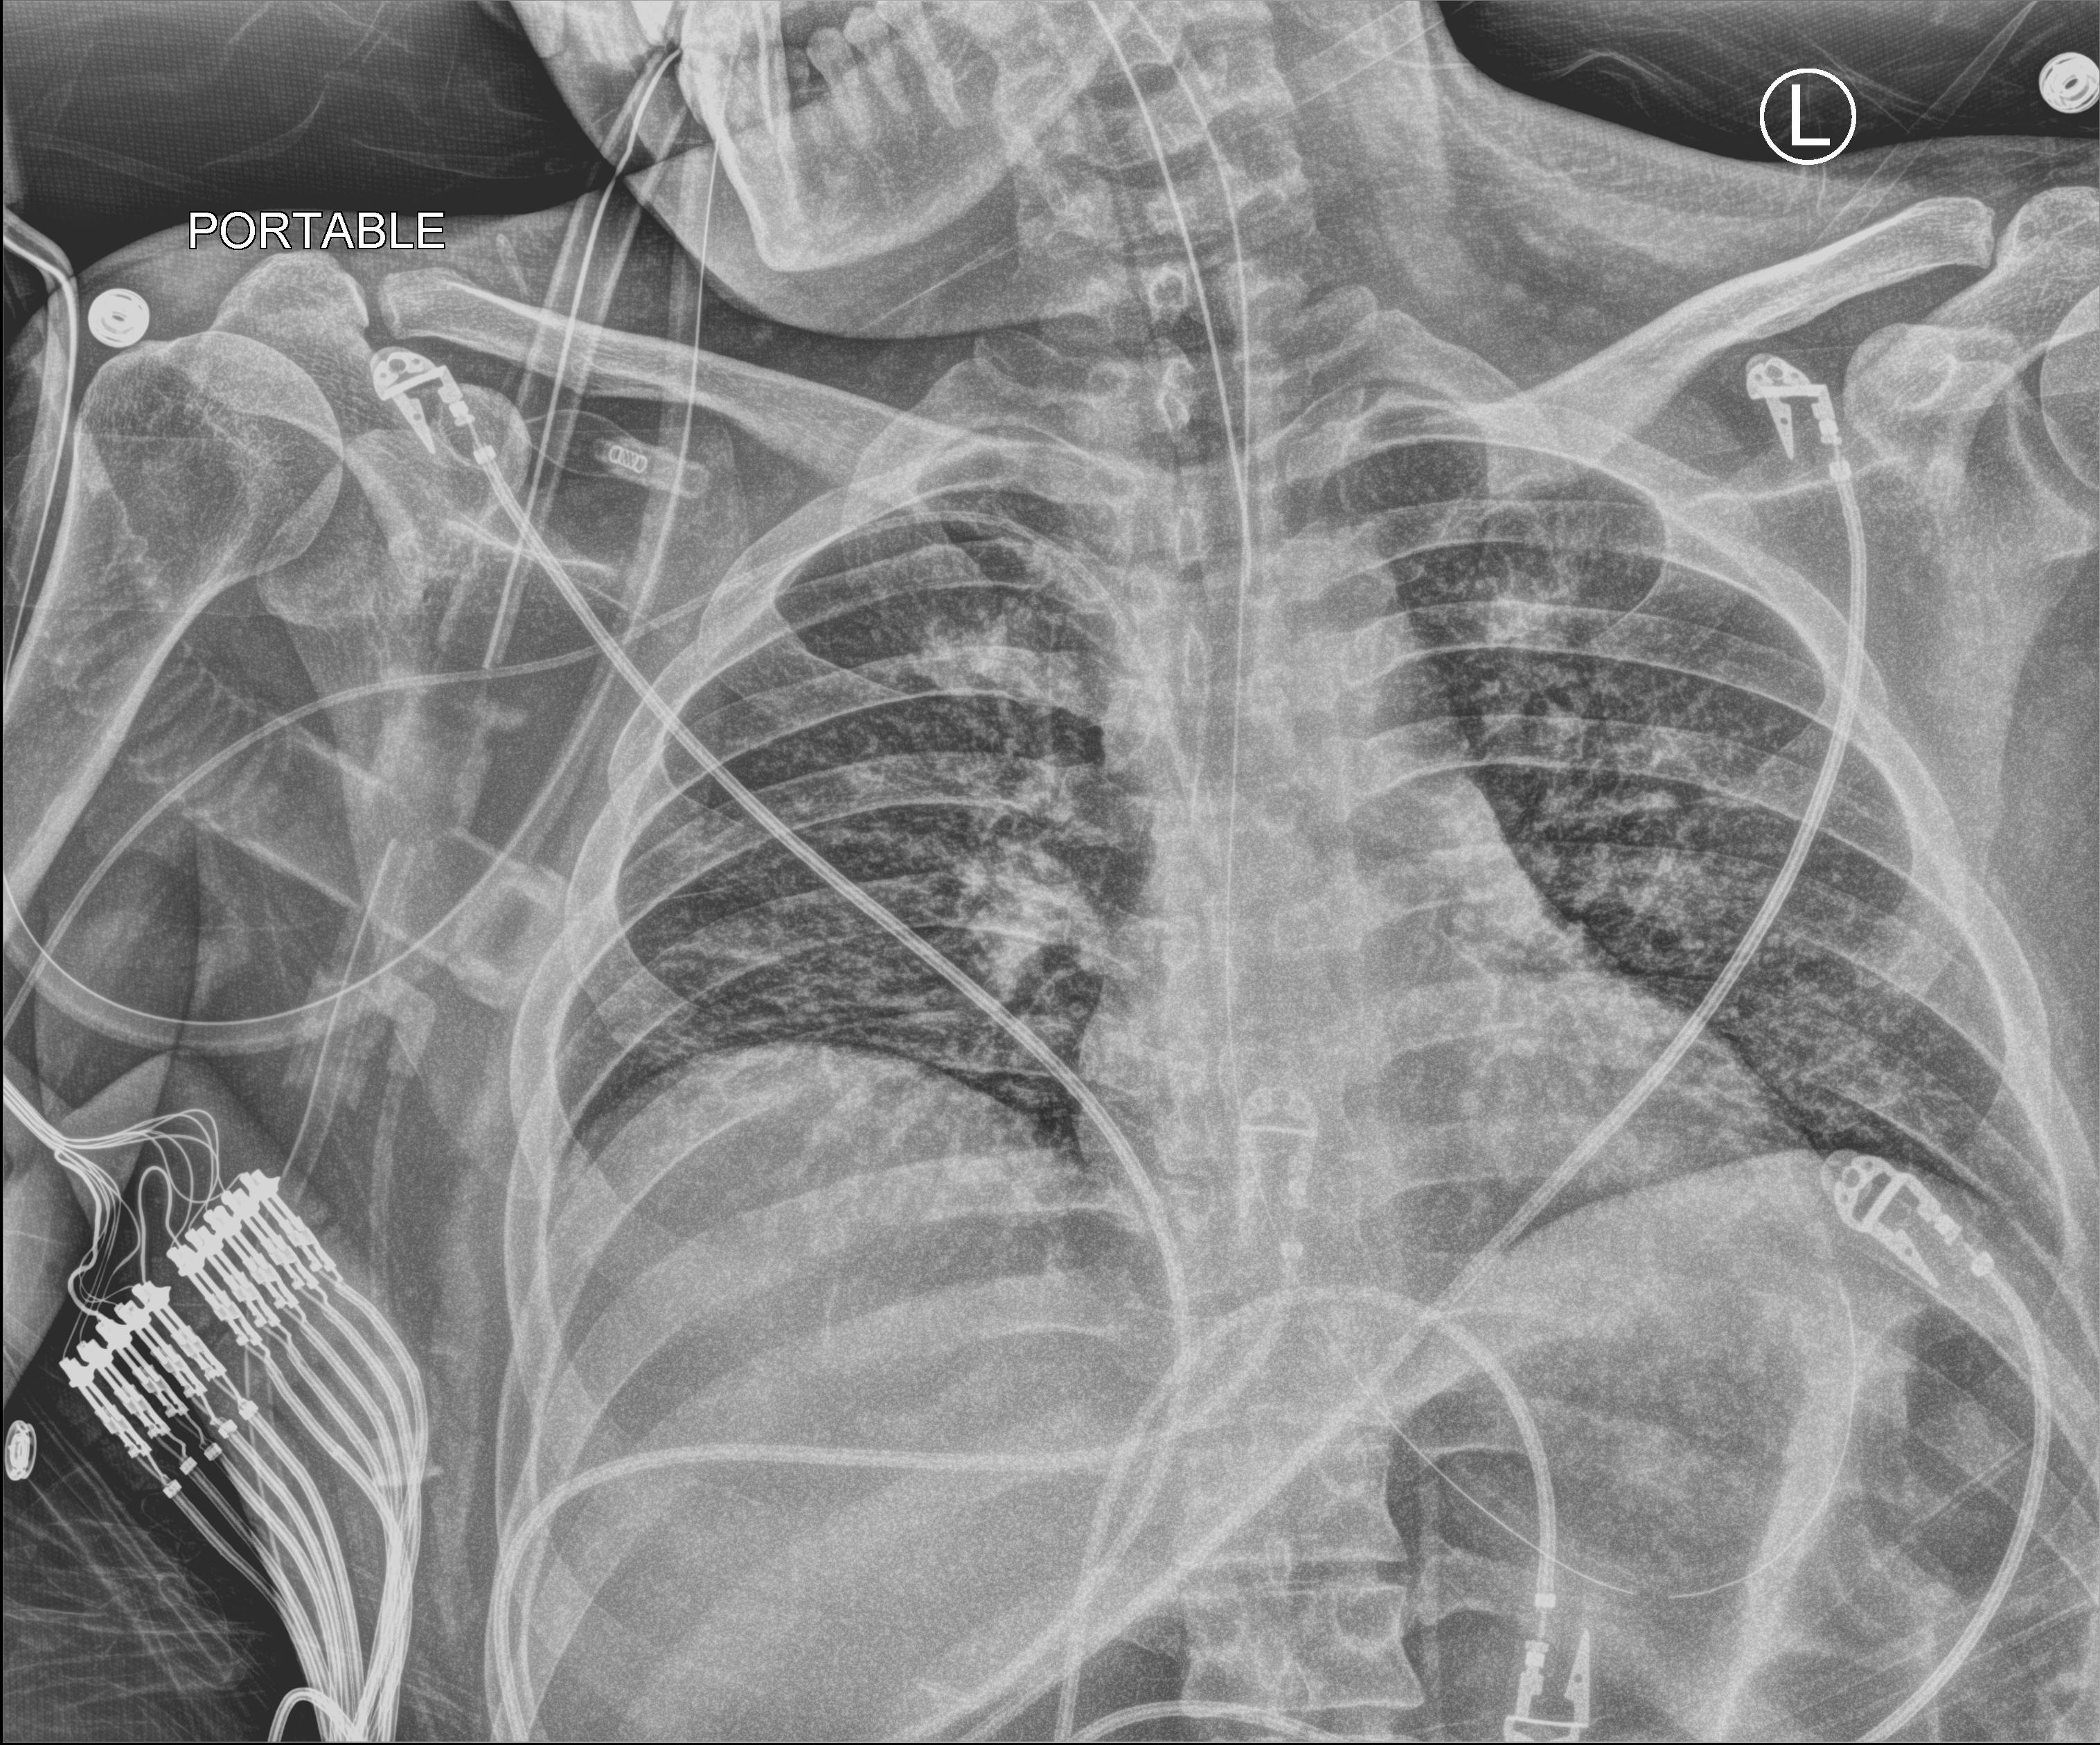
Chest X-ray (portable). Male patient hospitalised with COVID-19, age 18–59 years.
Admission-level facts for this patient (not findings on this image; timing relative to this image not recorded):
- hypertension (admission record): no
- COPD (admission record): no
- admitted to intensive care during this hospital stay: yes